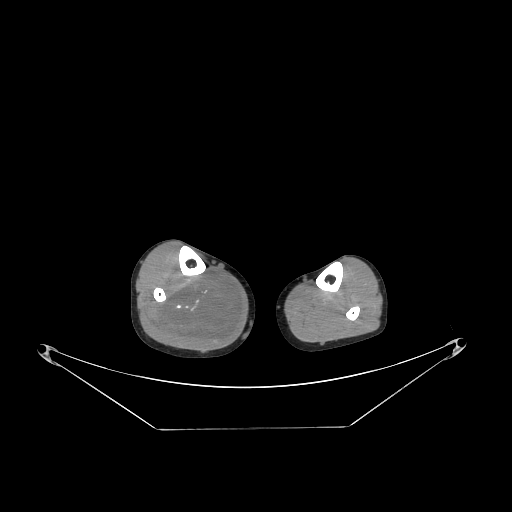
CT of an extremity soft-tissue mass (from a PET/CT study), one axial slice. Position 101 of 267 along the scan axis. 140 kVp. Soft-tissue window (W 400 / L 40 HU). 3.75 mm slice thickness. 512 × 512 image matrix, field of view 500 × 500 mm. Male patient. From the clinical record (not read from this slice): histological type: liposarcoma - round cell; grade: high; site of the primary tumour: right calf.
Annotated regions visible in this slice (expert contour drawn on MRI and transferred to this co-registered scan by the dataset authors):
- gross tumour volume (mass): bounding box (x1, y1, x2, y2) in pixels: (153, 272, 241, 344)